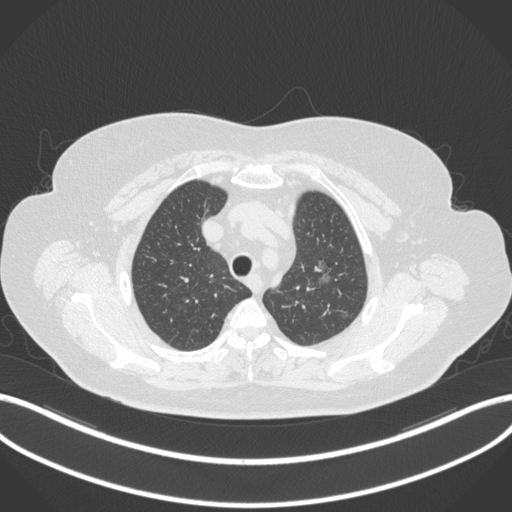
Chest CT, one axial slice; slice 271 of 310 in the series (ordered by position); reconstruction kernel B31f; lung window (W 1500 / L -600 HU); 1 mm slice thickness; 512 × 512 image matrix. Patient: female, 70 years. From the clinical record (not read from this slice): clinical TNM (as recorded): T1c N0 M0.
Annotated regions visible in this slice (bounding box drawn by a radiologist):
- lung tumour (recorded histology: adenocarcinoma): bounding box <312,258,334,289> (left, top, right, bottom; pixels)